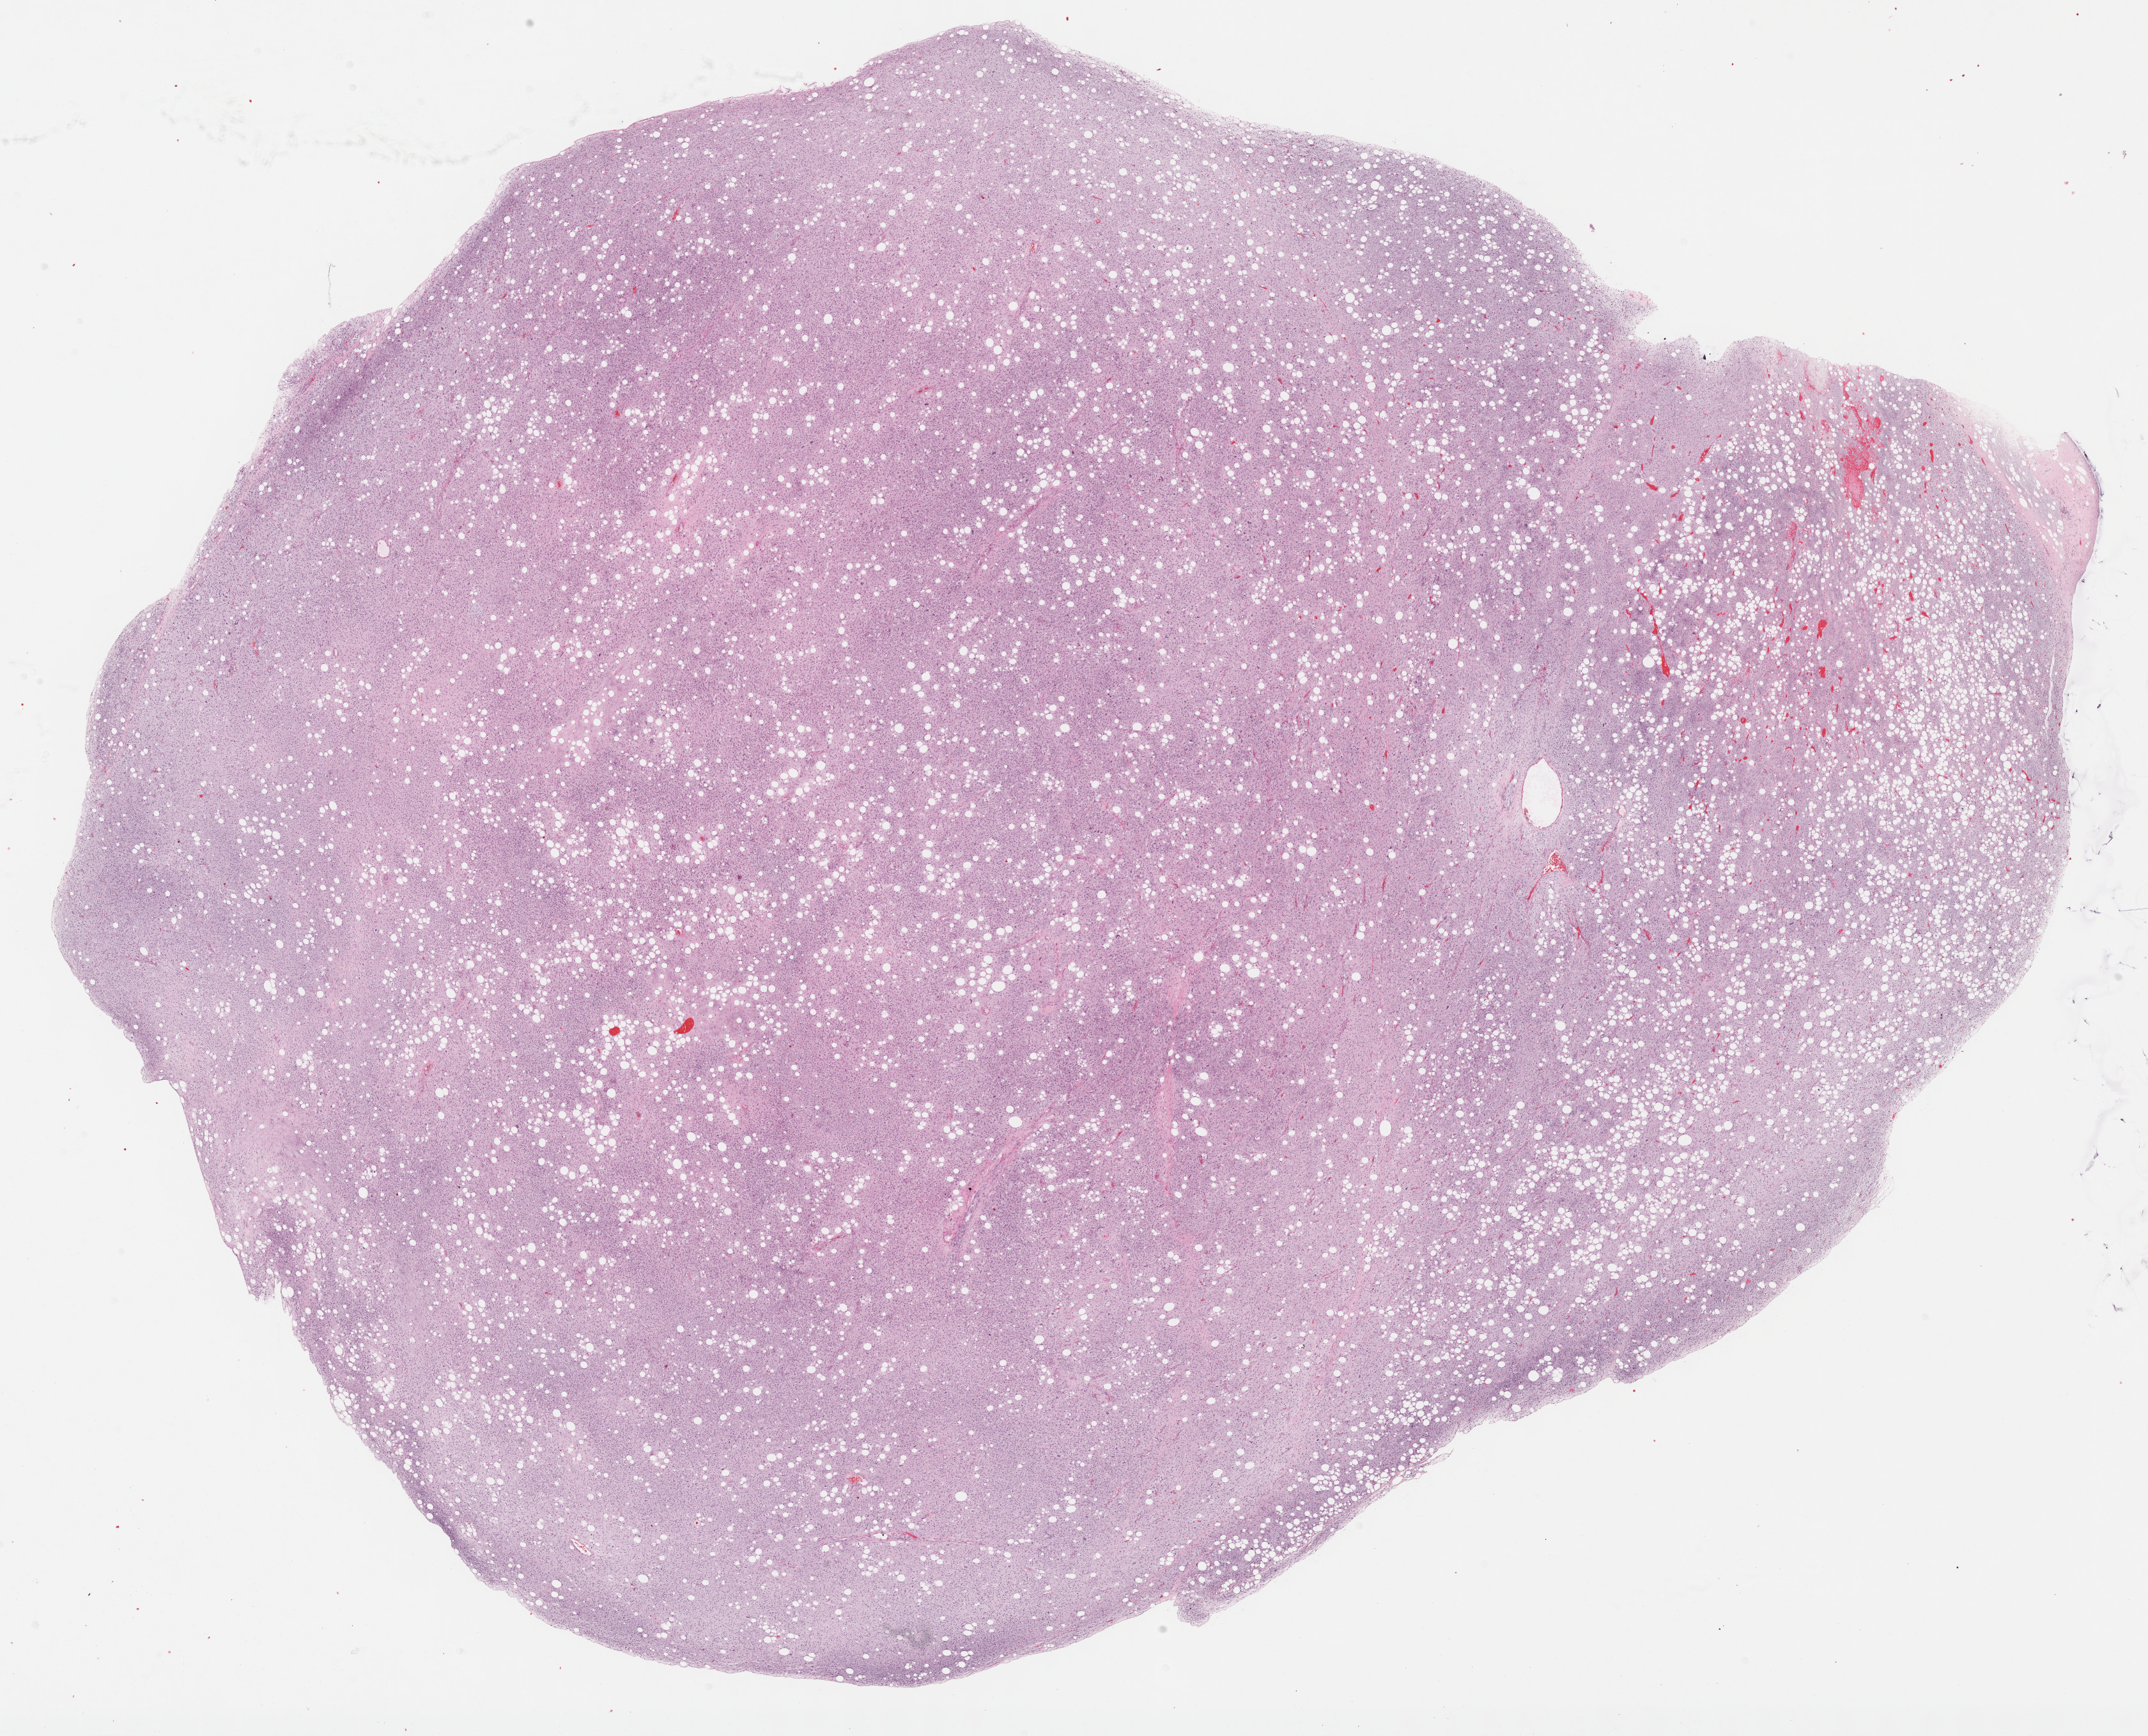
Hematoxylin and eosin (H&E) stained whole-slide image, whole scanned area (about 27.2 x 22.0 mm, acquisition: 40x scan) shown as a low-resolution overview, FFPE section, sample: primary tumour, retroperitoneum and peritoneum. Male, age 80 years at initial diagnosis.
Histologic diagnosis: Dedifferentiated liposarcoma (retroperitoneum).